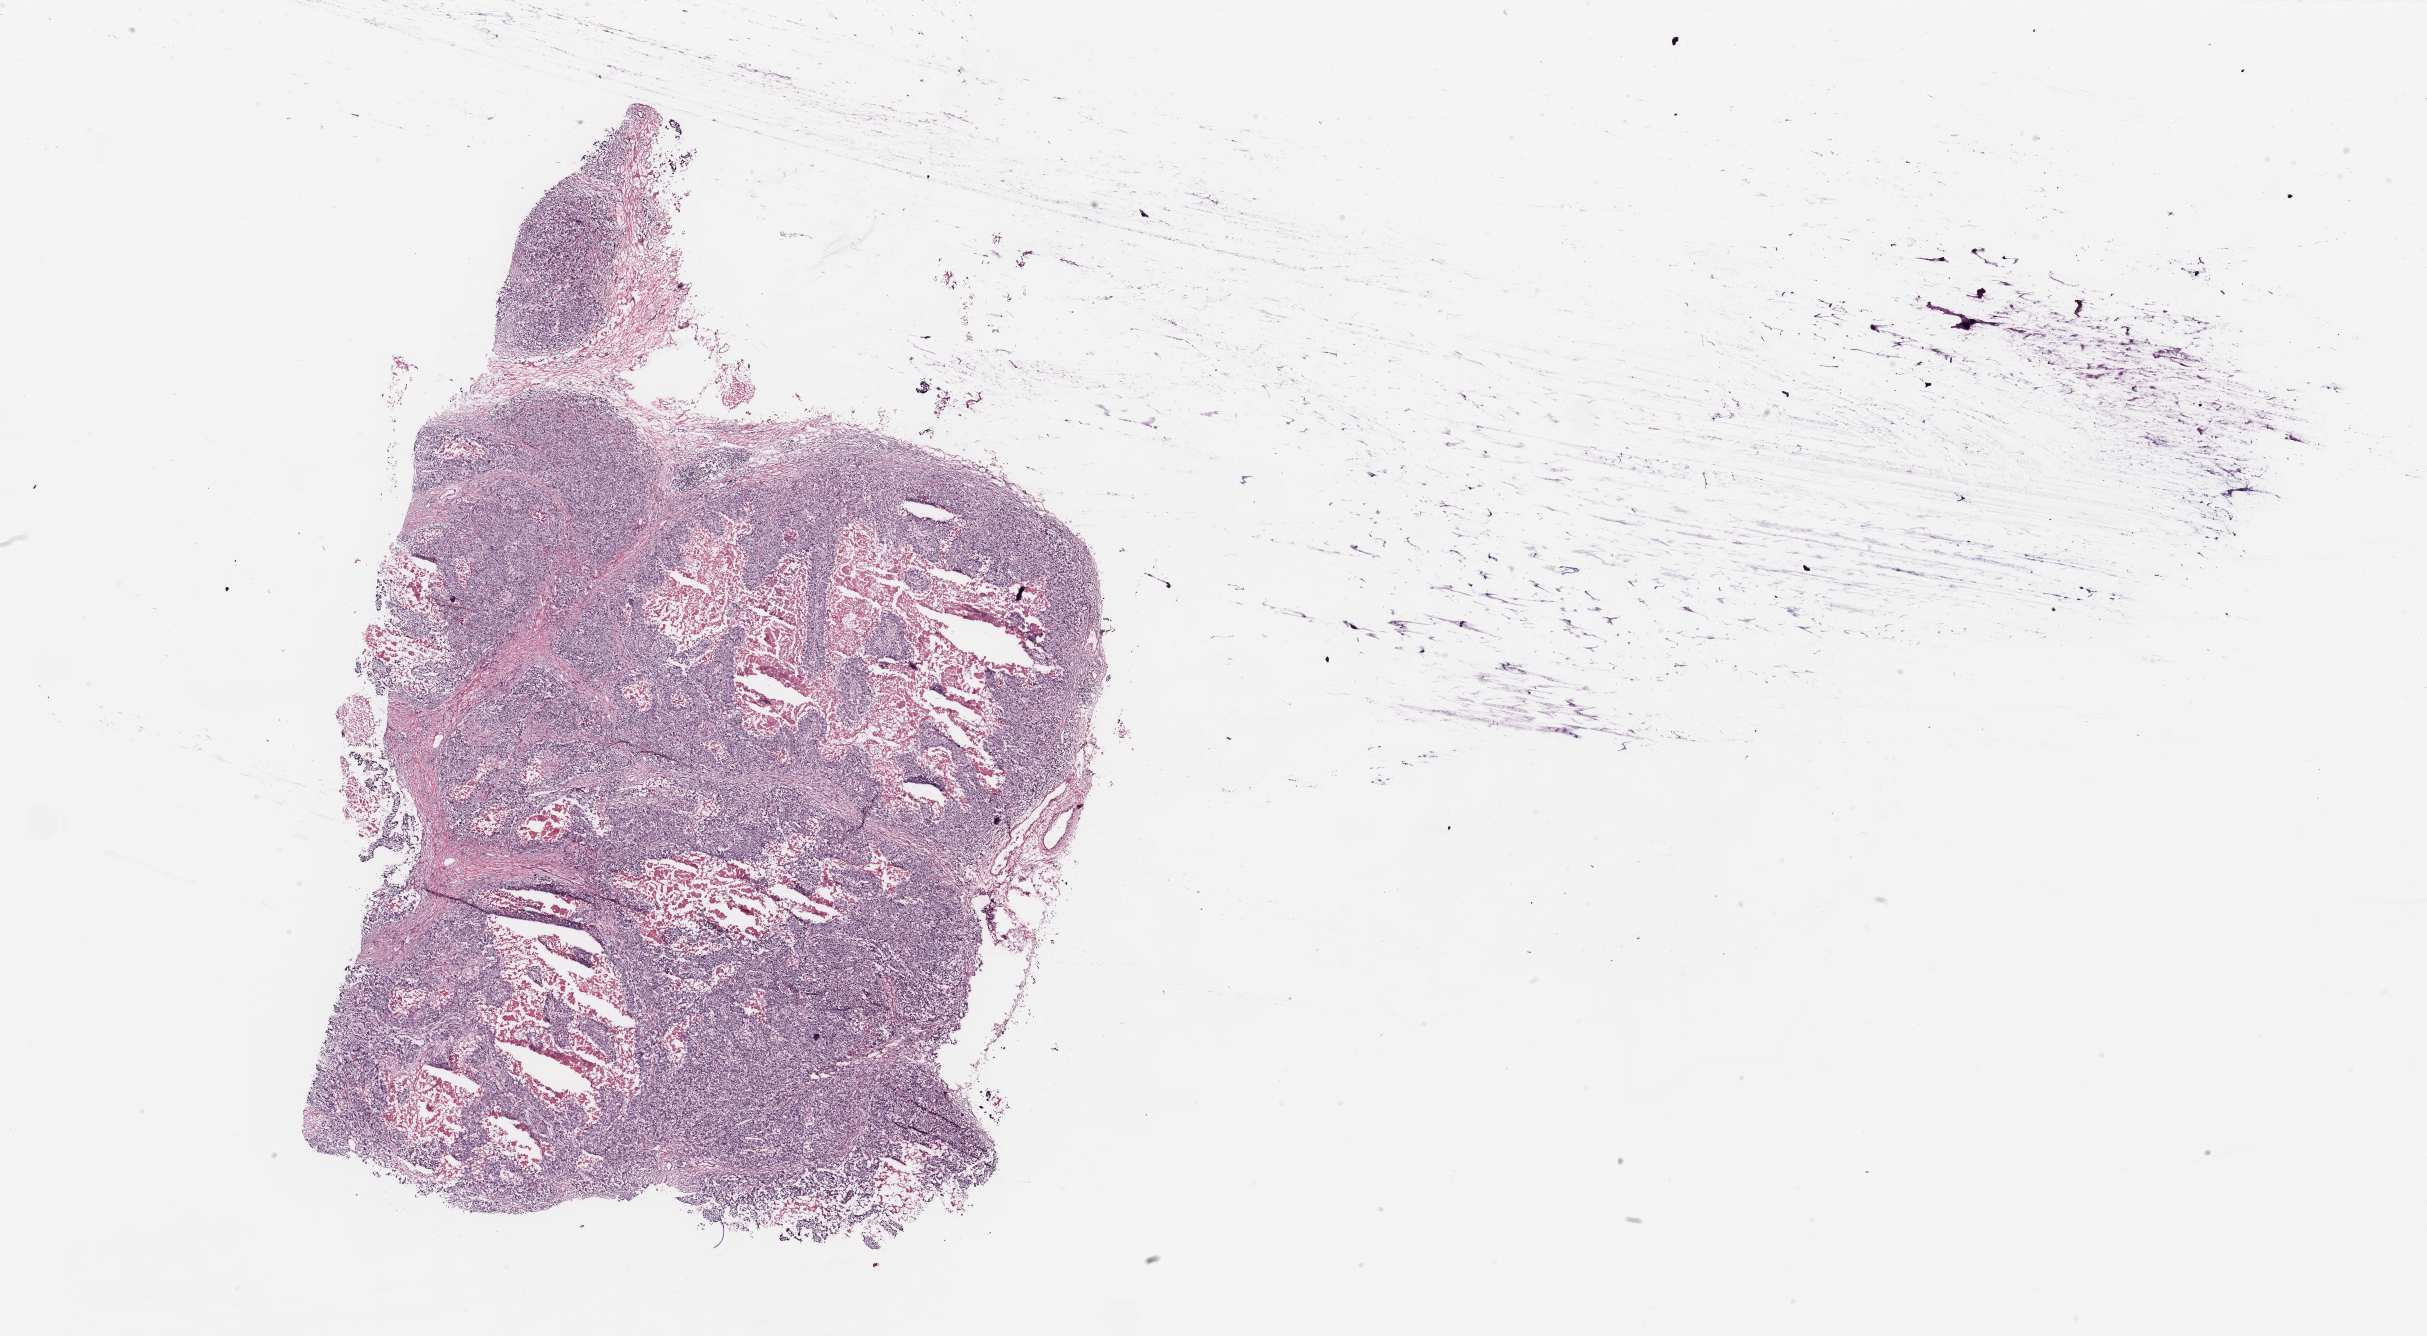
Digitized H&E tissue section (whole slide), low-resolution overview of the scanned area, about 38.4 x 21.1 mm (acquisition: 20x scan). Tumour tissue sample, breast. 75-year-old female patient.
* histologic diagnosis: Infiltrating duct carcinoma, NOS
* AJCC pathologic stage: IIA